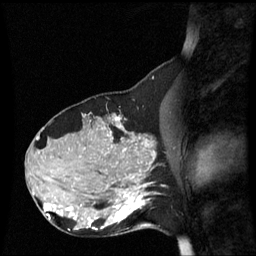
Breast MRI (dynamic contrast-enhanced), one sagittal slice; position 26 of 60 along the scan axis; dynamic contrast-enhanced series, image 2 of 3 at this slice position (ordered by acquisition); 1.5 T; TE 4.2 ms, TR 8.9 ms; 2.2 mm slice thickness; 256 × 256 image matrix, field of view 220 × 220 mm. Female patient, age 31 years. From the clinical record (not read from this slice): setting: breast cancer imaged before/during neoadjuvant chemotherapy; receptor status: HR-positive, HER2-negative.
Annotated regions visible in this slice (semi-automatic segmentation, software-assisted and operator-edited):
- analysis volume of interest (the breast-tissue region the enhancement analysis was run in; not a lesion): bounding box (x1, y1, x2, y2) in pixels: (90, 180, 152, 237)
- tumour enhancement mask (voxels above the 70 % enhancement threshold inside the analysis volume of interest): (90, 180, 150, 231)